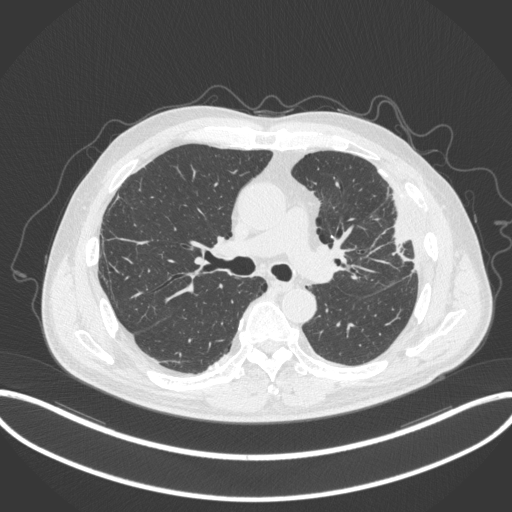
Chest CT, one axial slice; 120 kVp; lung window (W 1500 / L -600 HU); 512 × 512 image matrix, field of view 415 × 415 mm. Male patient, age 64 years. Case-level facts recorded for this patient, not image findings: clinical TNM (as recorded): T4 N1 M0; histopathological grade: G3.
Structures marked on this image (bounding box drawn by a radiologist):
- lung tumour (recorded histology: adenocarcinoma): bounding box (x1, y1, x2, y2) in pixels: (380, 185, 415, 264)